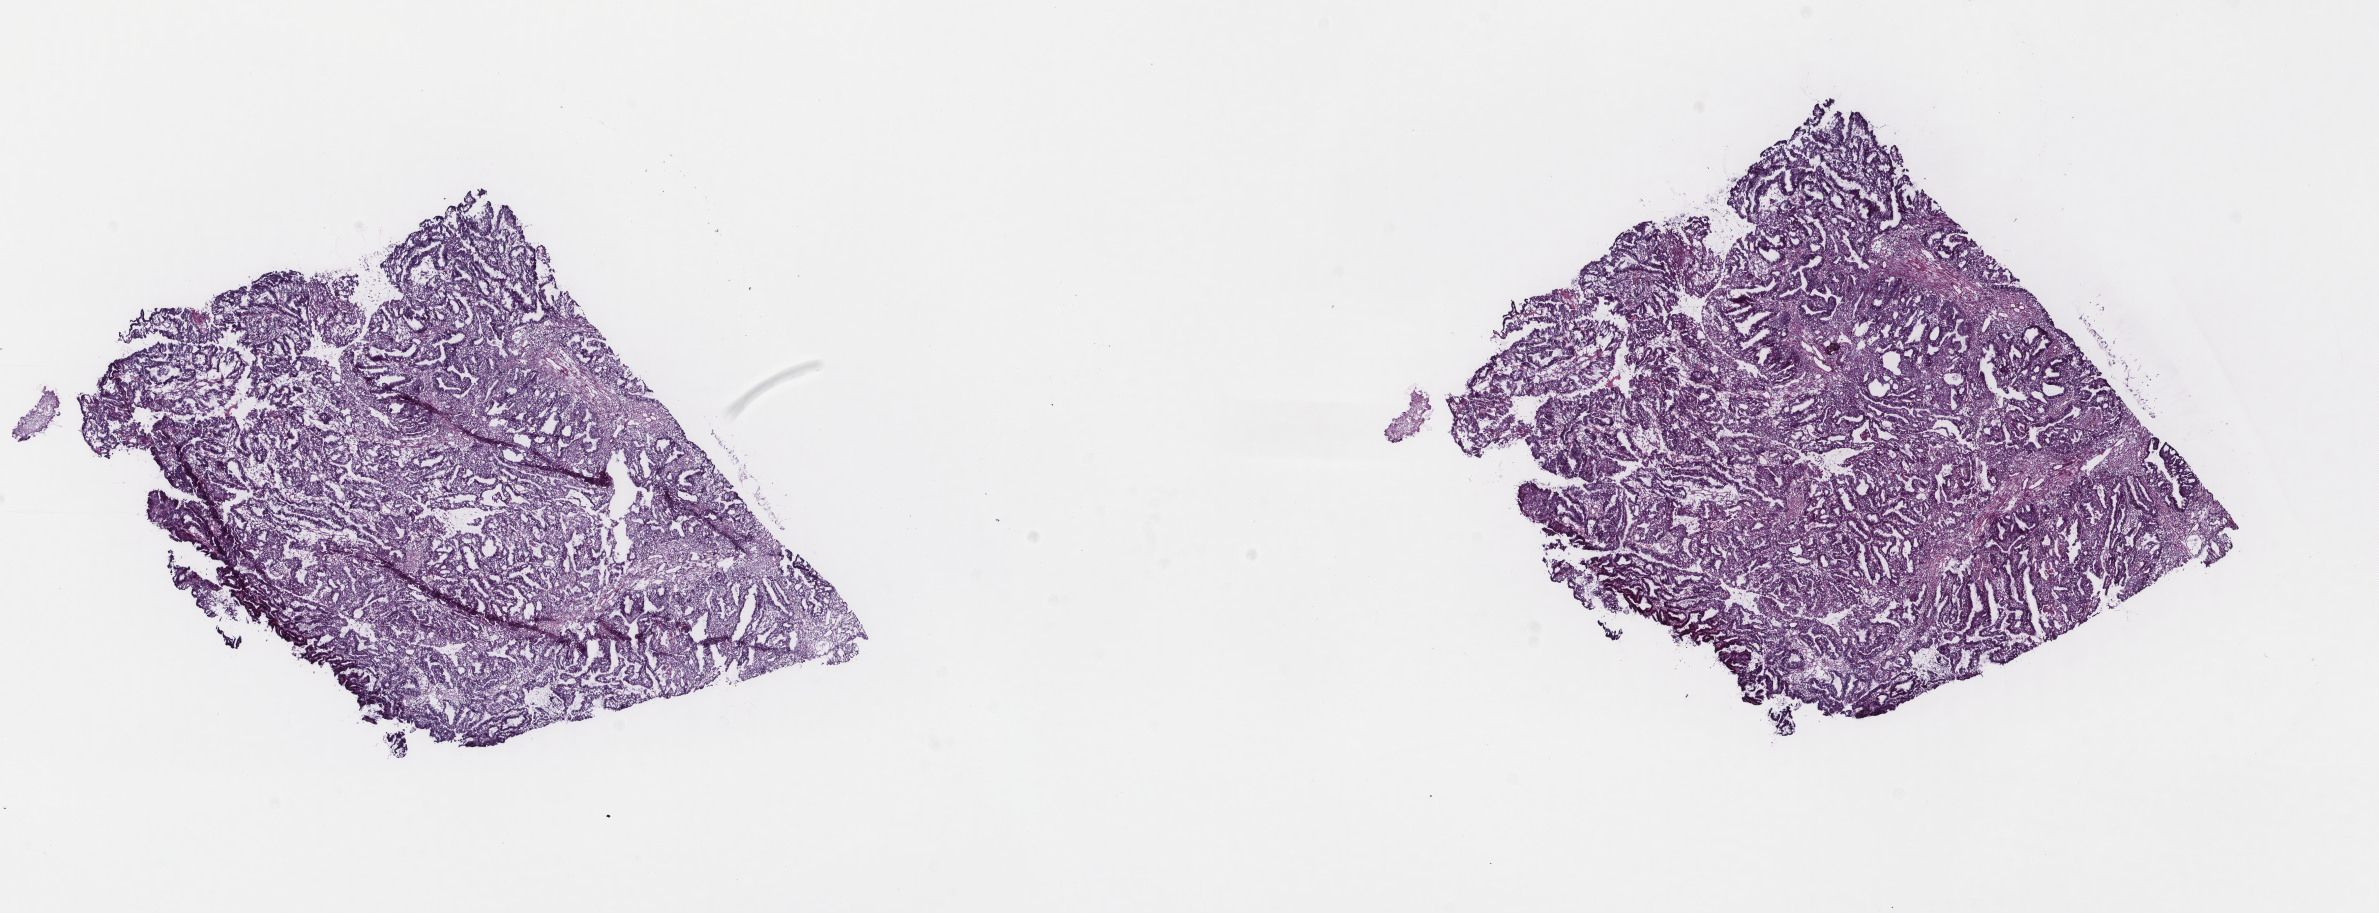
H&E whole-slide image — whole scanned area (about 18.9 x 7.2 mm) shown as a low-resolution overview. Frozen section. Uterus, primary tumour sample. Female patient; age at initial diagnosis 56 years. Histologic grade: G1 (well differentiated). Pathologist review of this section (percent, as recorded): tumour cells 65%, tumour nuclei 65%, normal cells 0%, stromal cells 35%, necrosis 0%. Infiltration values recorded for this section: lymphocyte infiltration 10%, monocyte infiltration 2%, neutrophil infiltration 3%.
FIGO stage: II. Diagnosis: Endometrioid adenocarcinoma, NOS (endometrium).